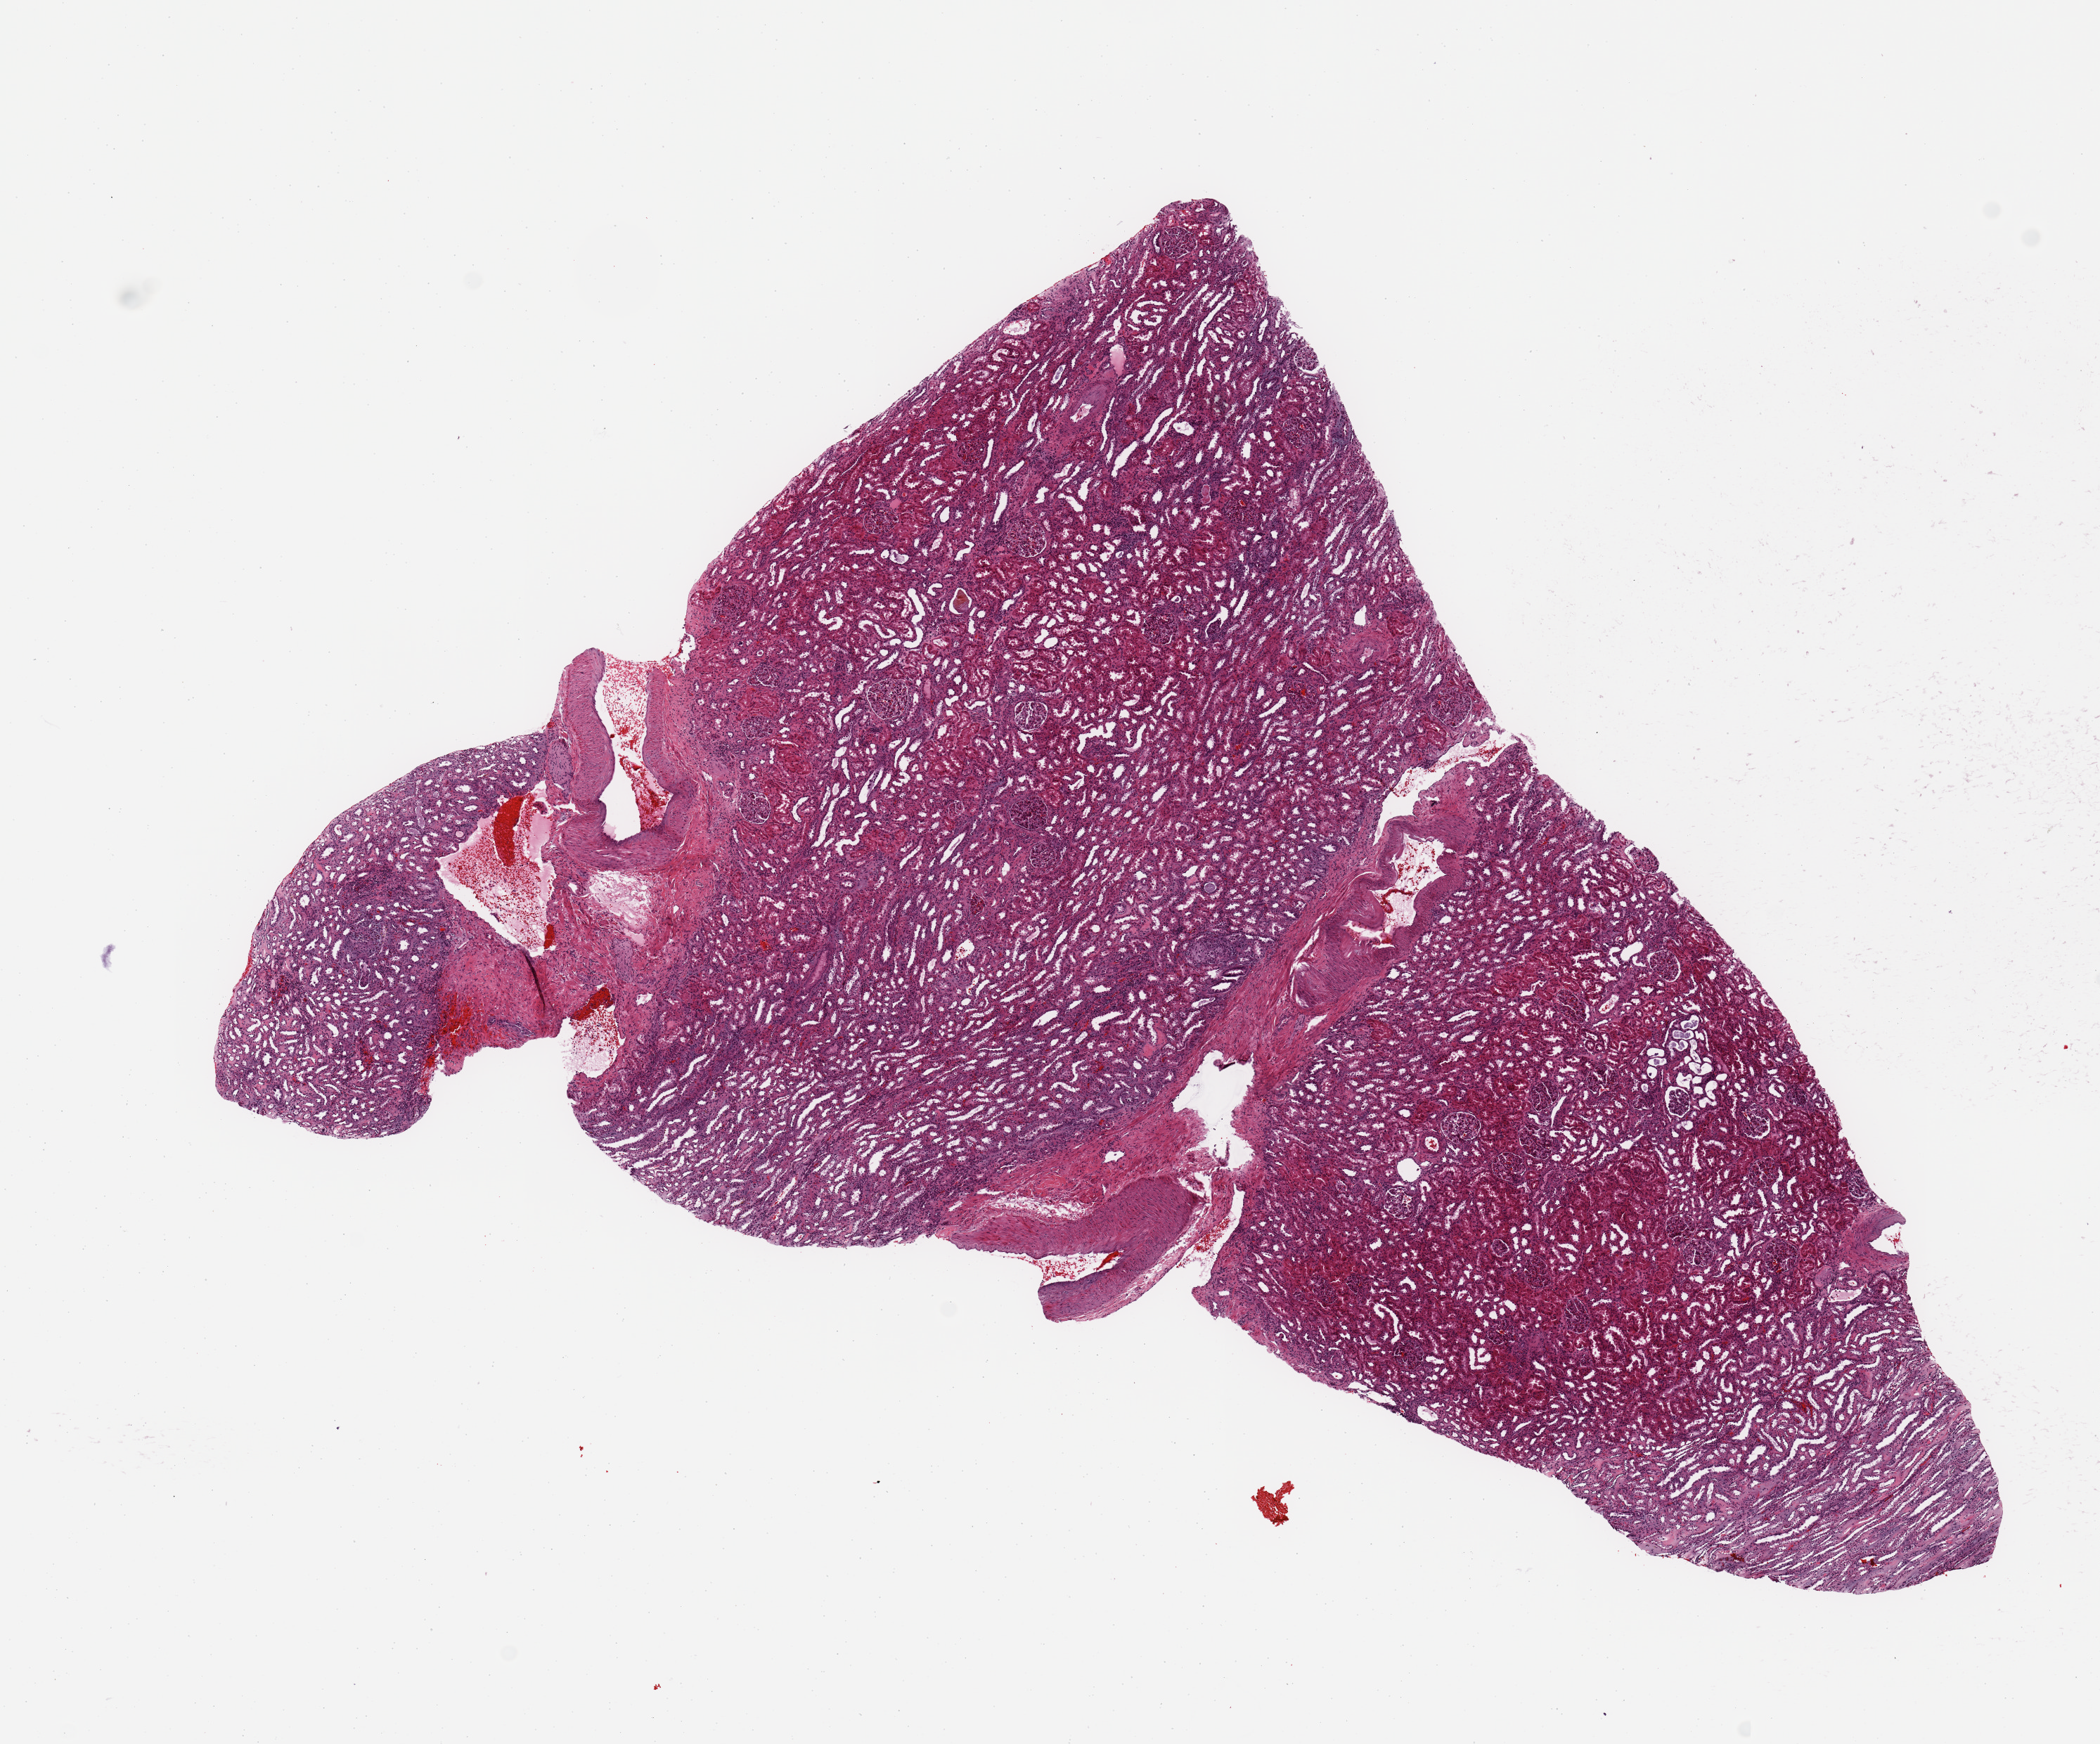
Whole-slide histology image, H&E-stained, shown as a low-resolution overview of the whole scanned area (about 11.8 x 9.8 mm); normal (non-tumour) tissue sample, sampled site: kidney. 52-year-old male patient.
• this section: normal (non-tumour) tissue from the same patient
• patient diagnosis: Renal cell carcinoma, NOS